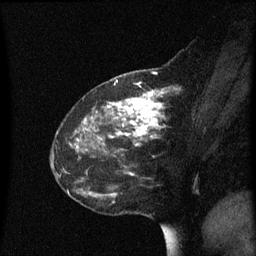
Breast MRI (dynamic contrast-enhanced), one sagittal slice. Slice 23 of 60 in the series (ordered by position). Dynamic contrast-enhanced series, image 2 of 3 at this slice position (ordered by acquisition). 1.5 T. TE 4.2 ms, TR 8.4 ms. 2 mm slice thickness. 256 × 256 image matrix, field of view 200 × 200 mm. Female patient, age 48 years. Case-level facts recorded for this patient, not image findings: setting: breast cancer imaged before/during neoadjuvant chemotherapy; receptor status: HR-positive, HER2-negative.
Structures marked on this image (semi-automatic segmentation, software-assisted and operator-edited):
- analysis volume of interest (the breast-tissue region the enhancement analysis was run in; not a lesion): box from (x=80, y=78) to (x=195, y=218) px
- tumour enhancement mask (voxels above the 70 % enhancement threshold inside the analysis volume of interest): (x=100, y=81)–(x=165, y=147)